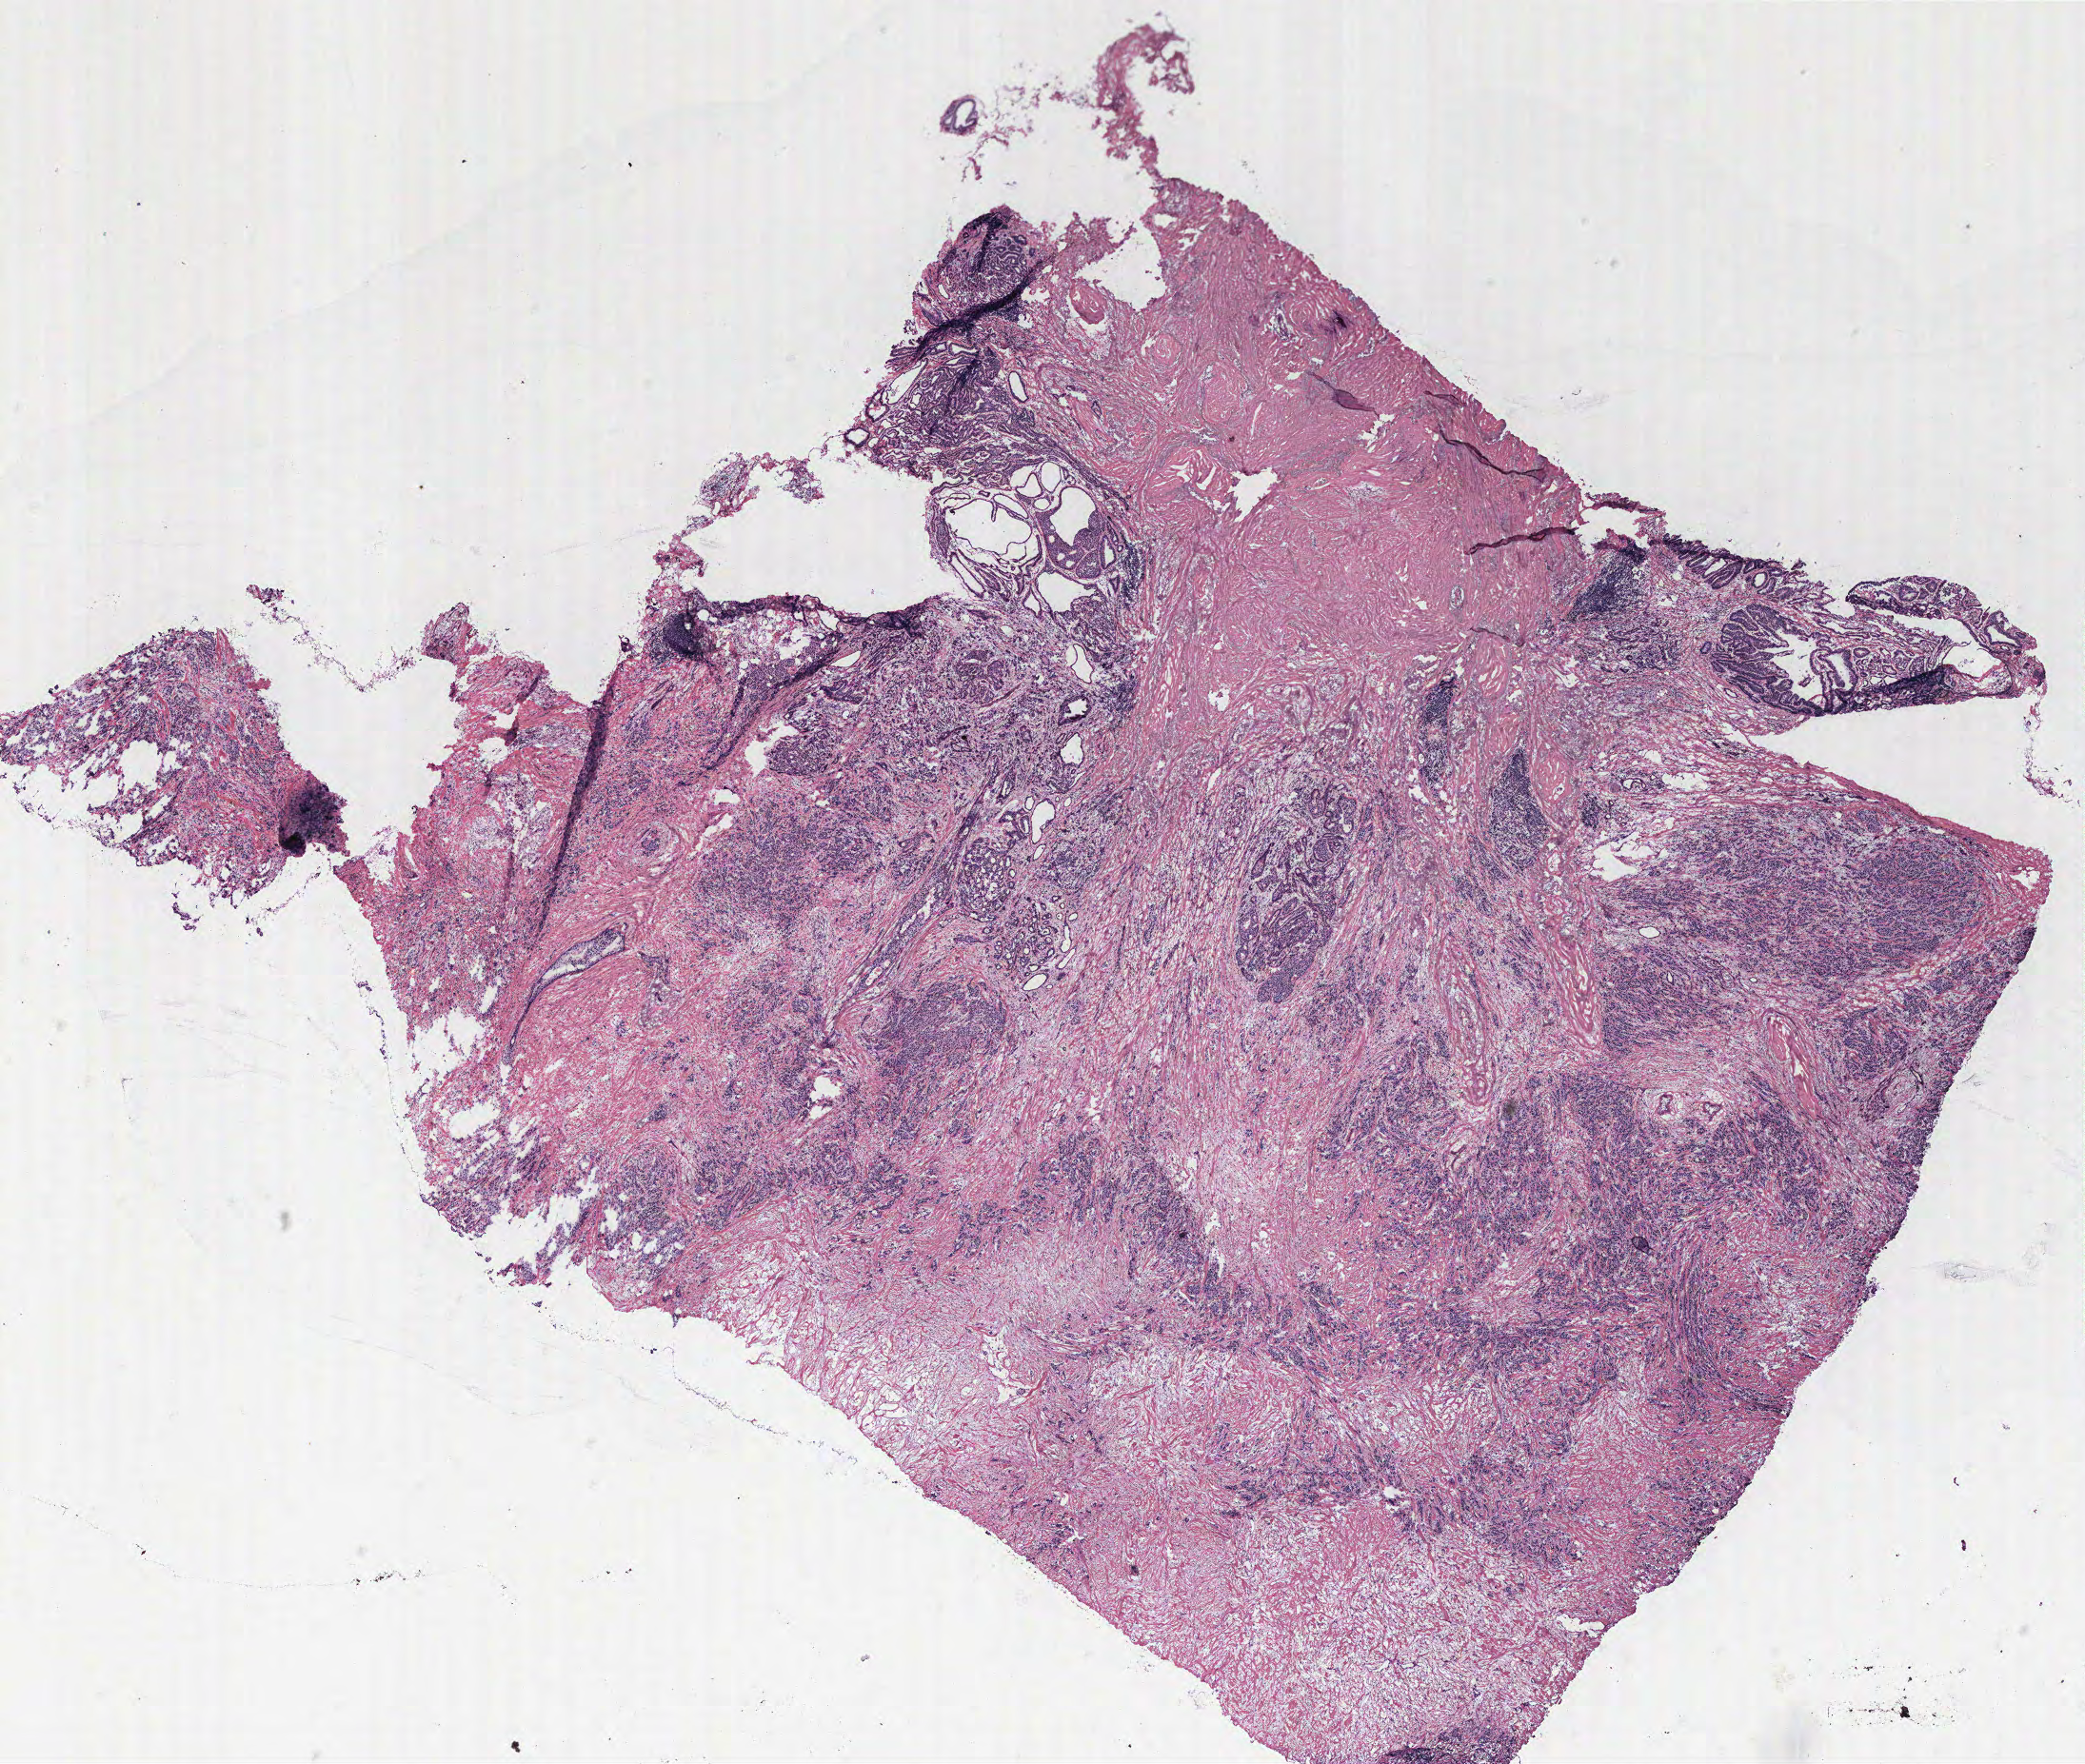
Digitized H&E tissue section (whole slide) — low-resolution overview of the scanned area, about 17.5 x 14.8 mm (acquisition: 40x scan); breast, tumour tissue. Female, 64 y/o.
Diagnosis: Infiltrating duct carcinoma, NOS.